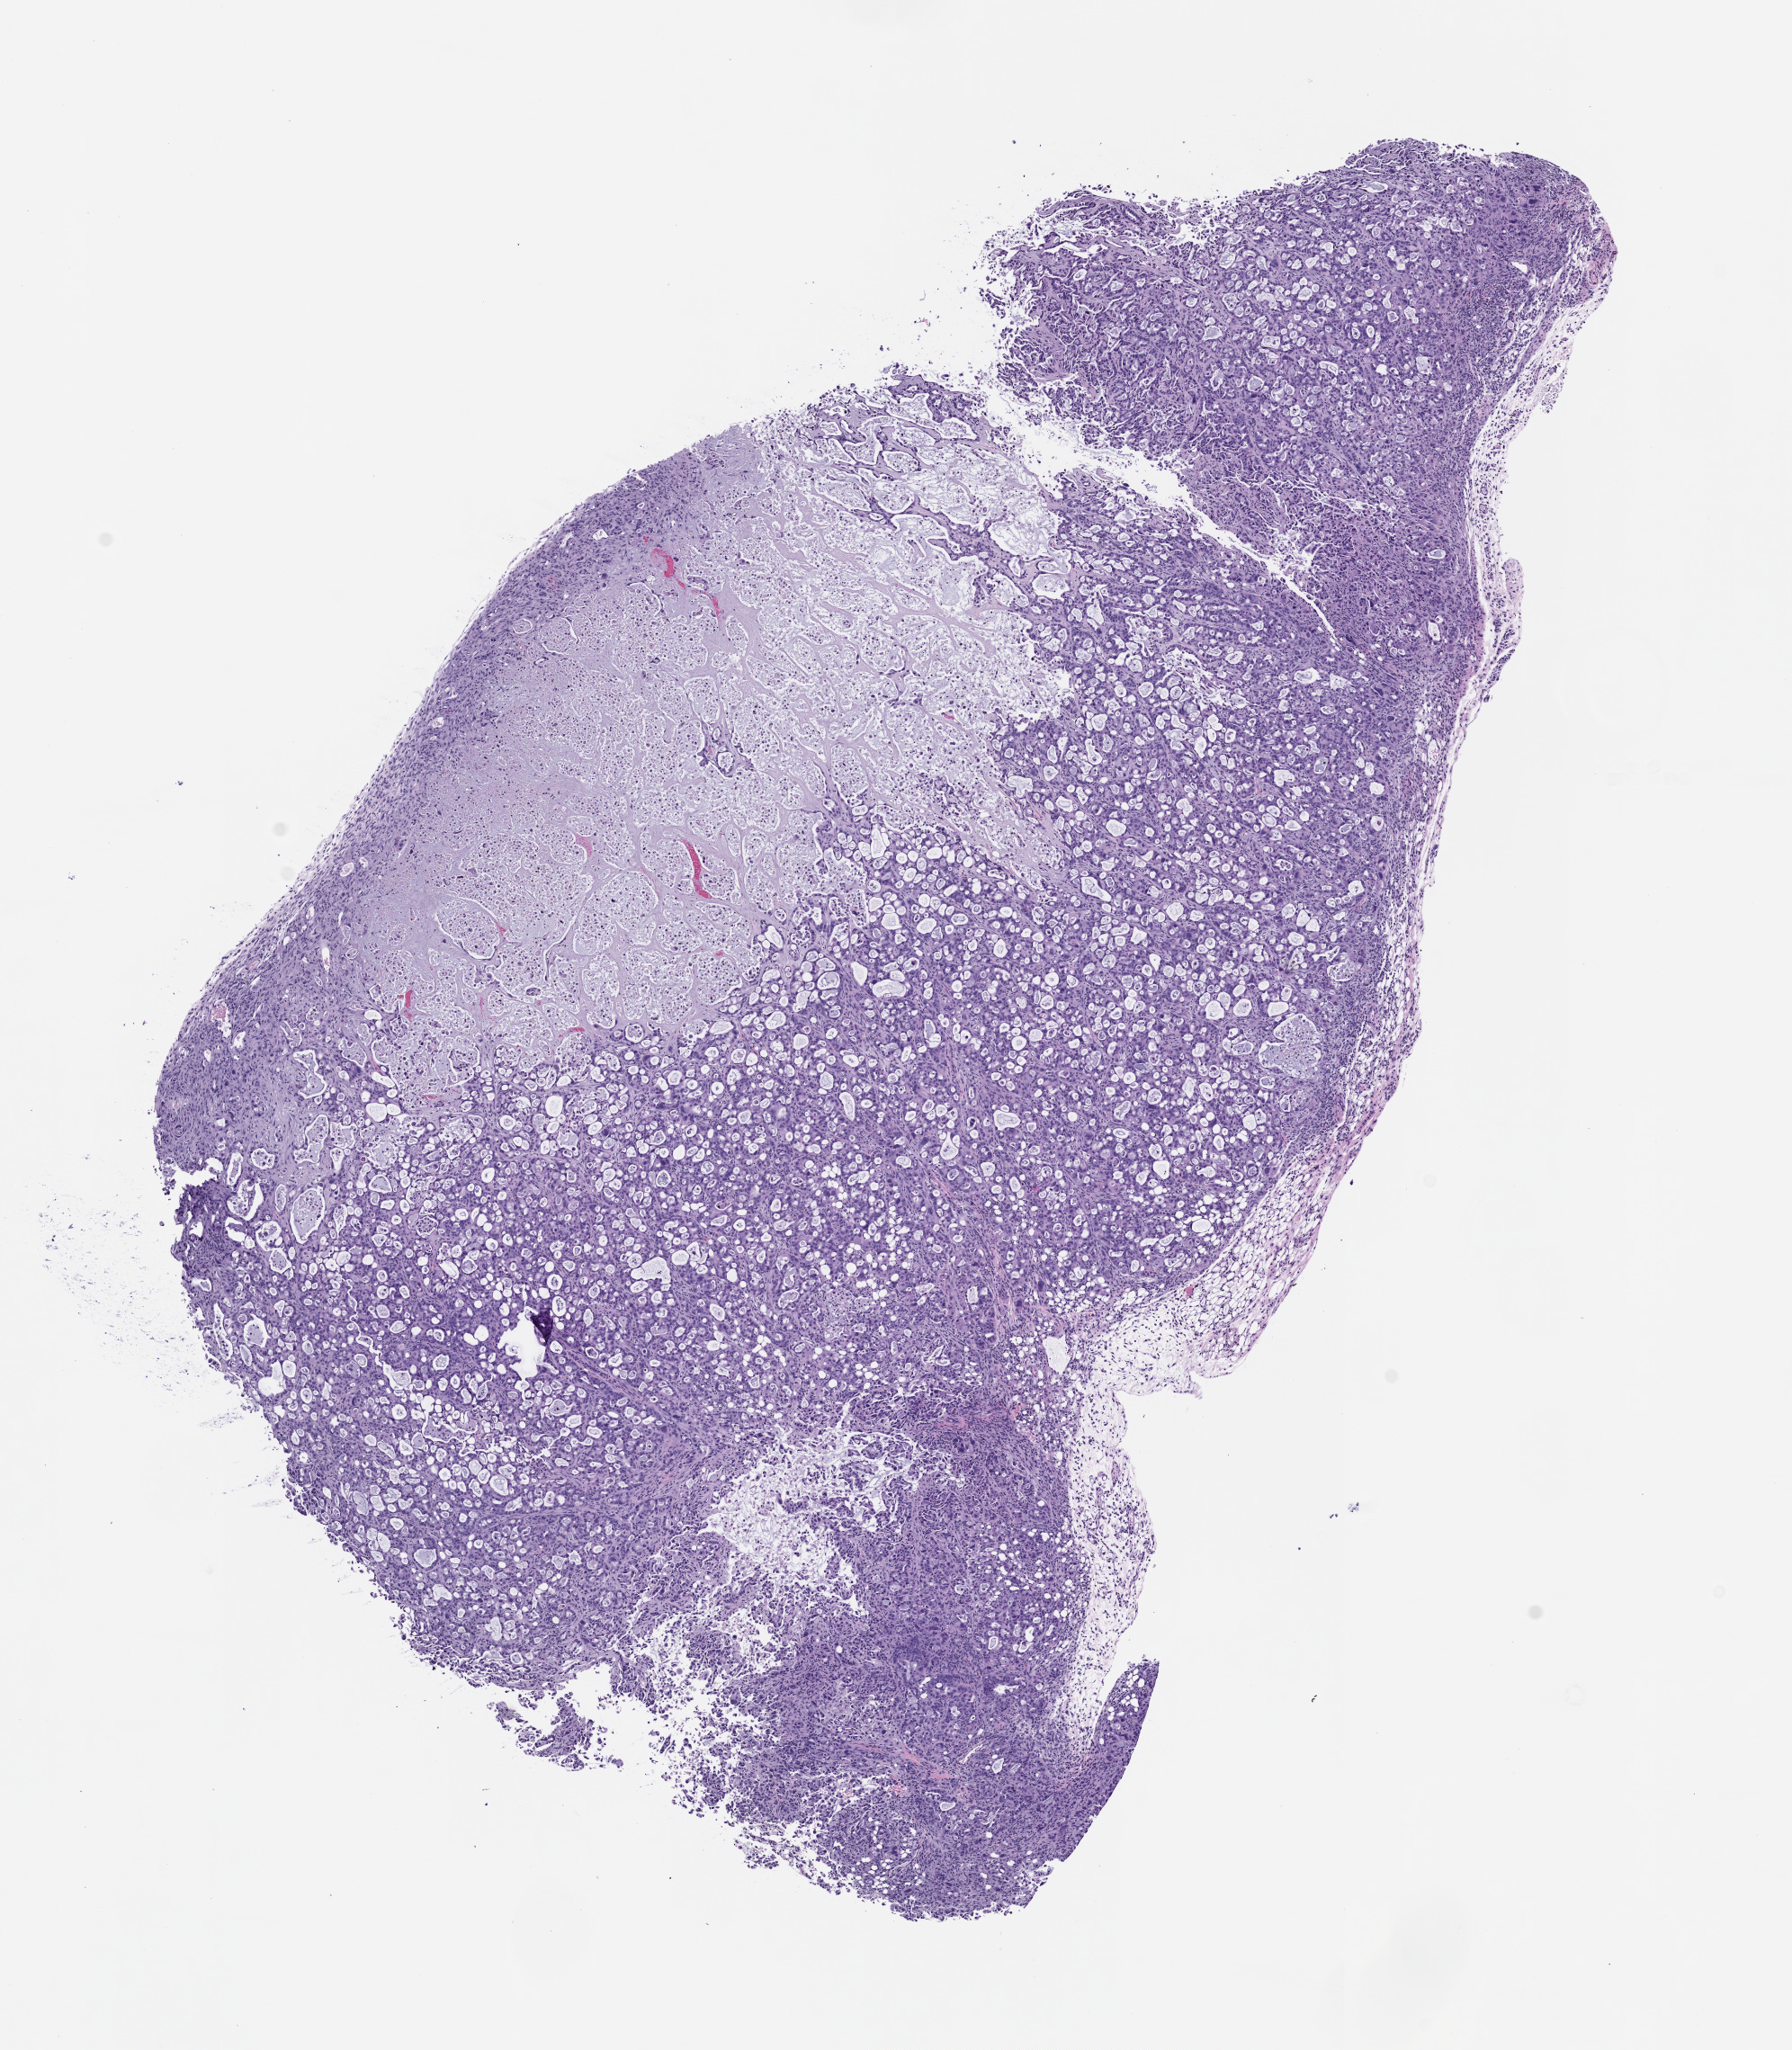
Haematoxylin and eosin whole-slide image of a patient-derived xenograft (PDX) tumor grown in a mouse, passage 1 — a low-resolution overview of the entire scanned area, about 8.0 x 9.2 mm; formalin-fixed paraffin-embedded section; tumor site category: pancreas.
Originating patient diagnosis: Pancreatic Adenocarcinoma.